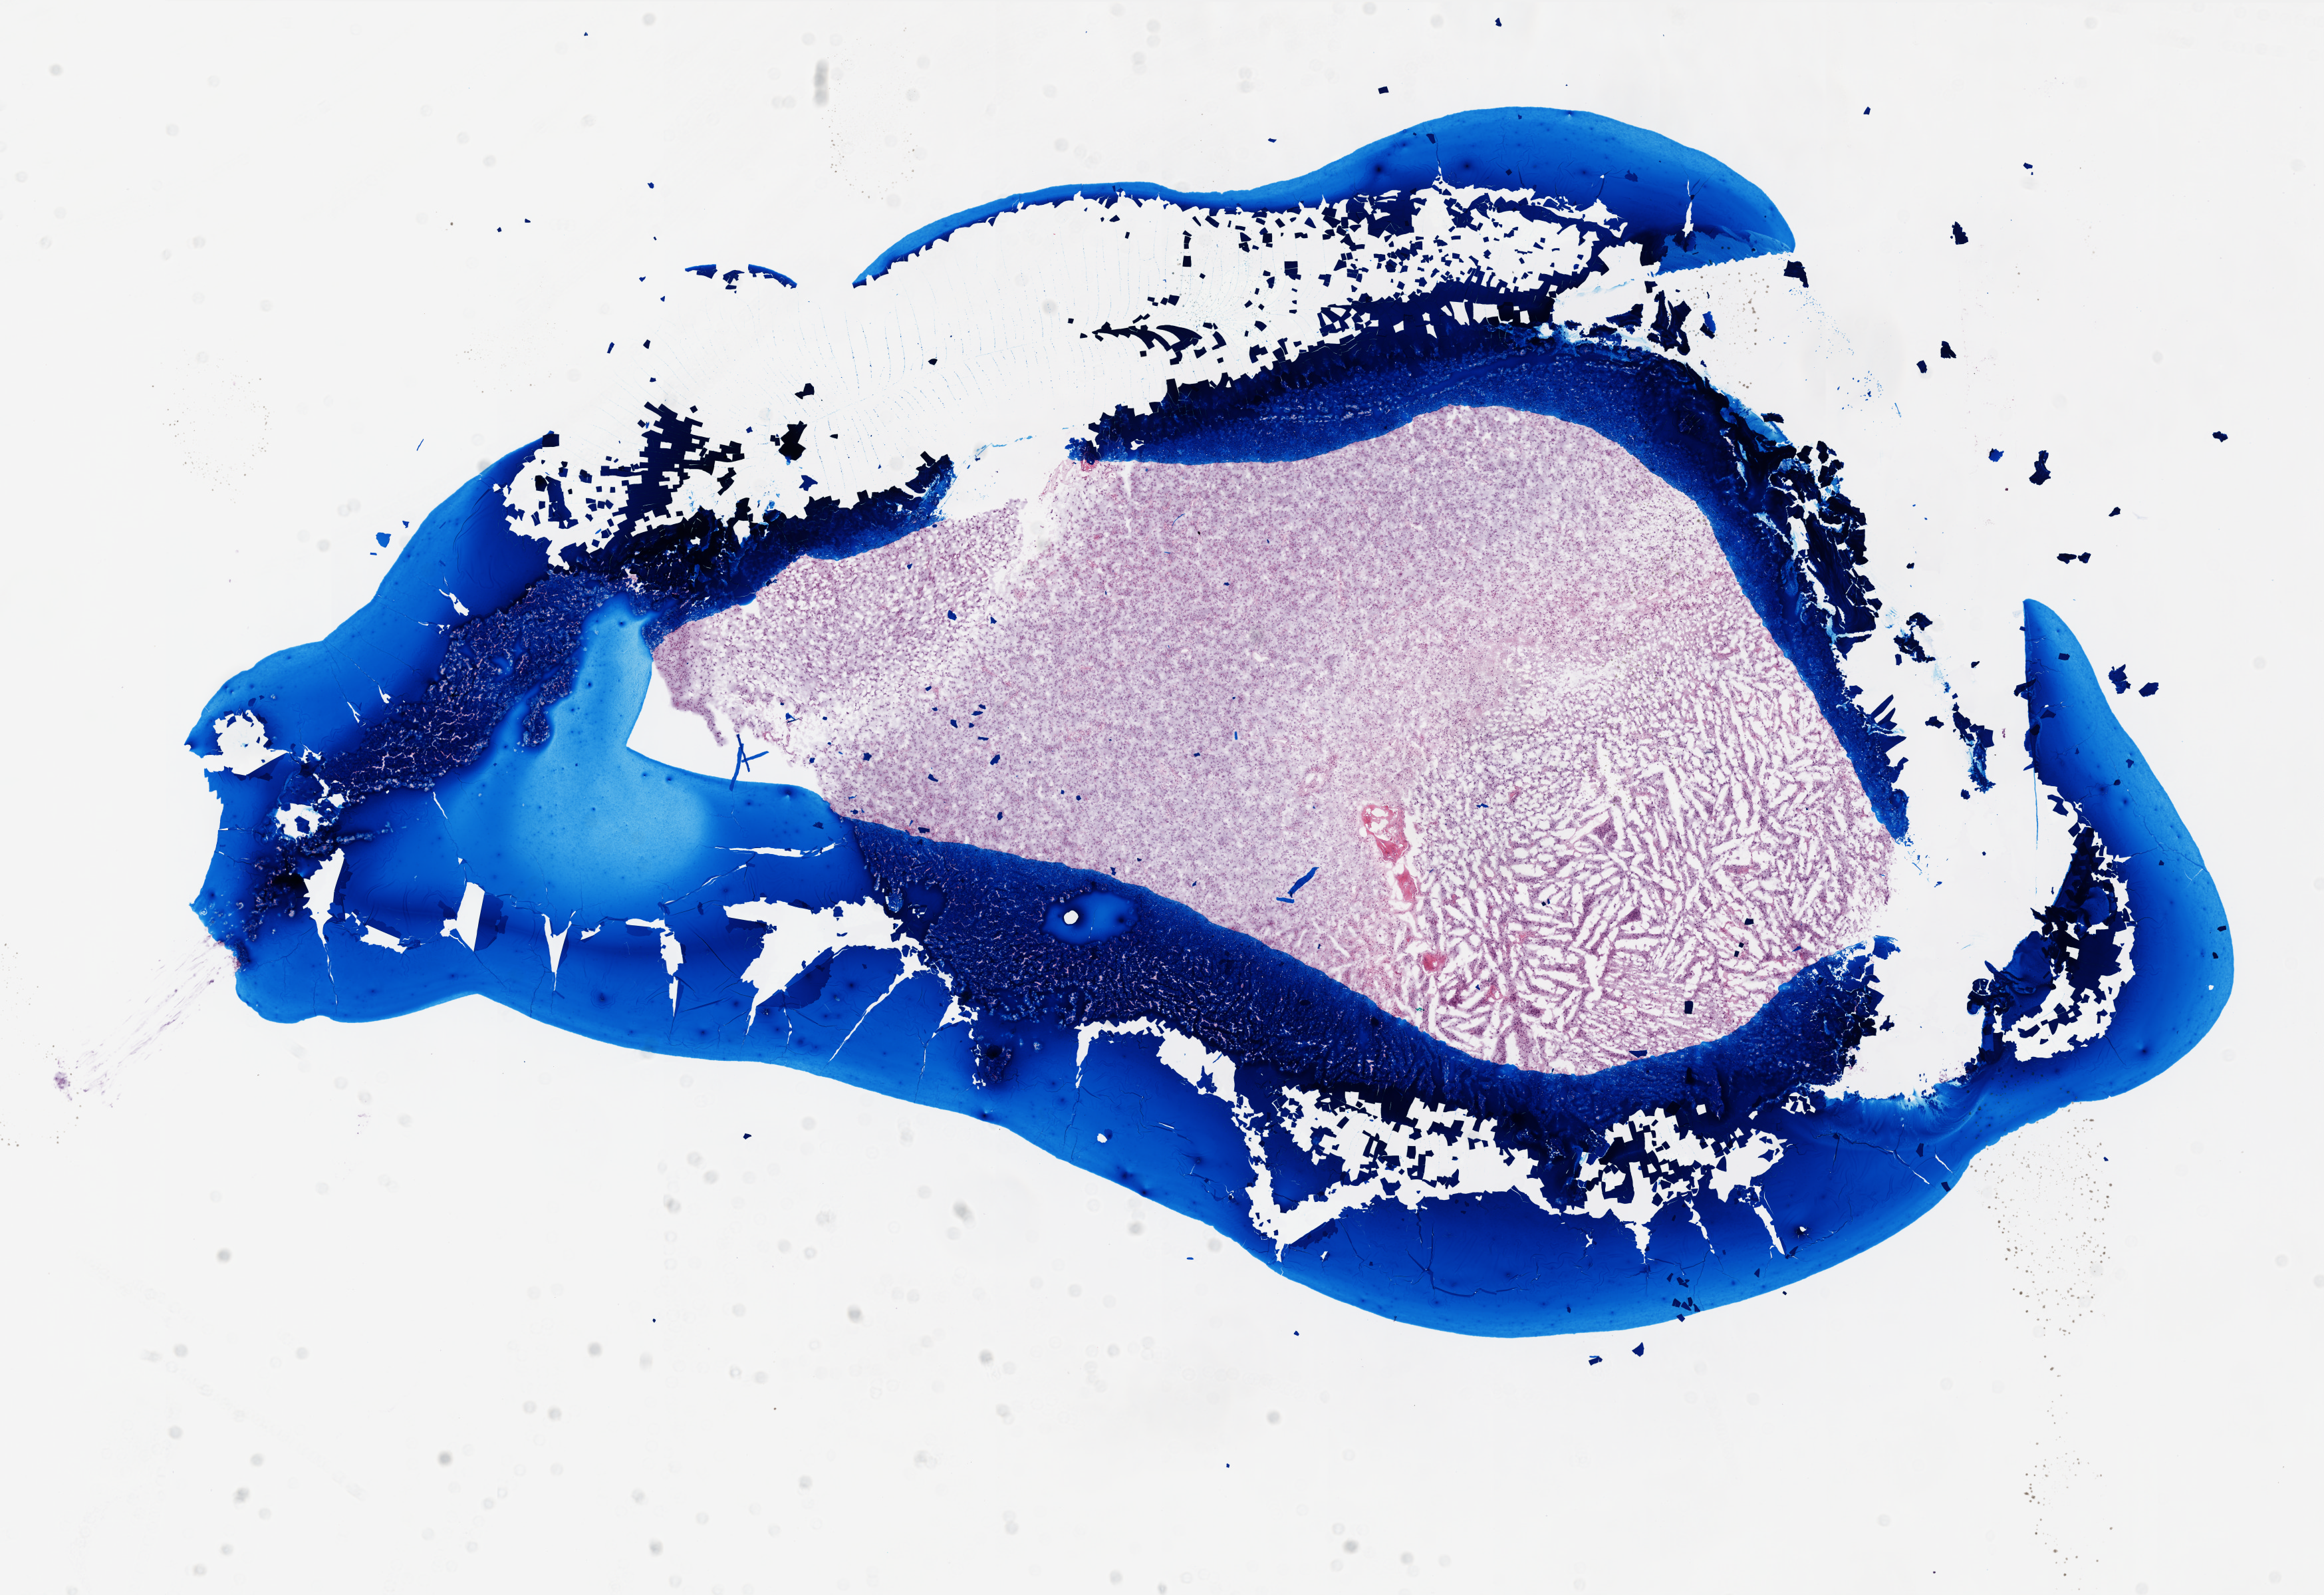
Whole-slide histology image, H&E-stained, shown as a low-resolution overview of the whole scanned area (about 14.0 x 9.6 mm), frozen section from the top of the tissue portion, primary tumour sample from the brain. Female, age 18 years at initial diagnosis. Pathologist review of this section (percent, as recorded): tumour cells 95%, tumour nuclei 100%, normal cells 0%, stromal cells 0%, necrosis 5%.
Pathologic diagnosis: Glioblastoma.